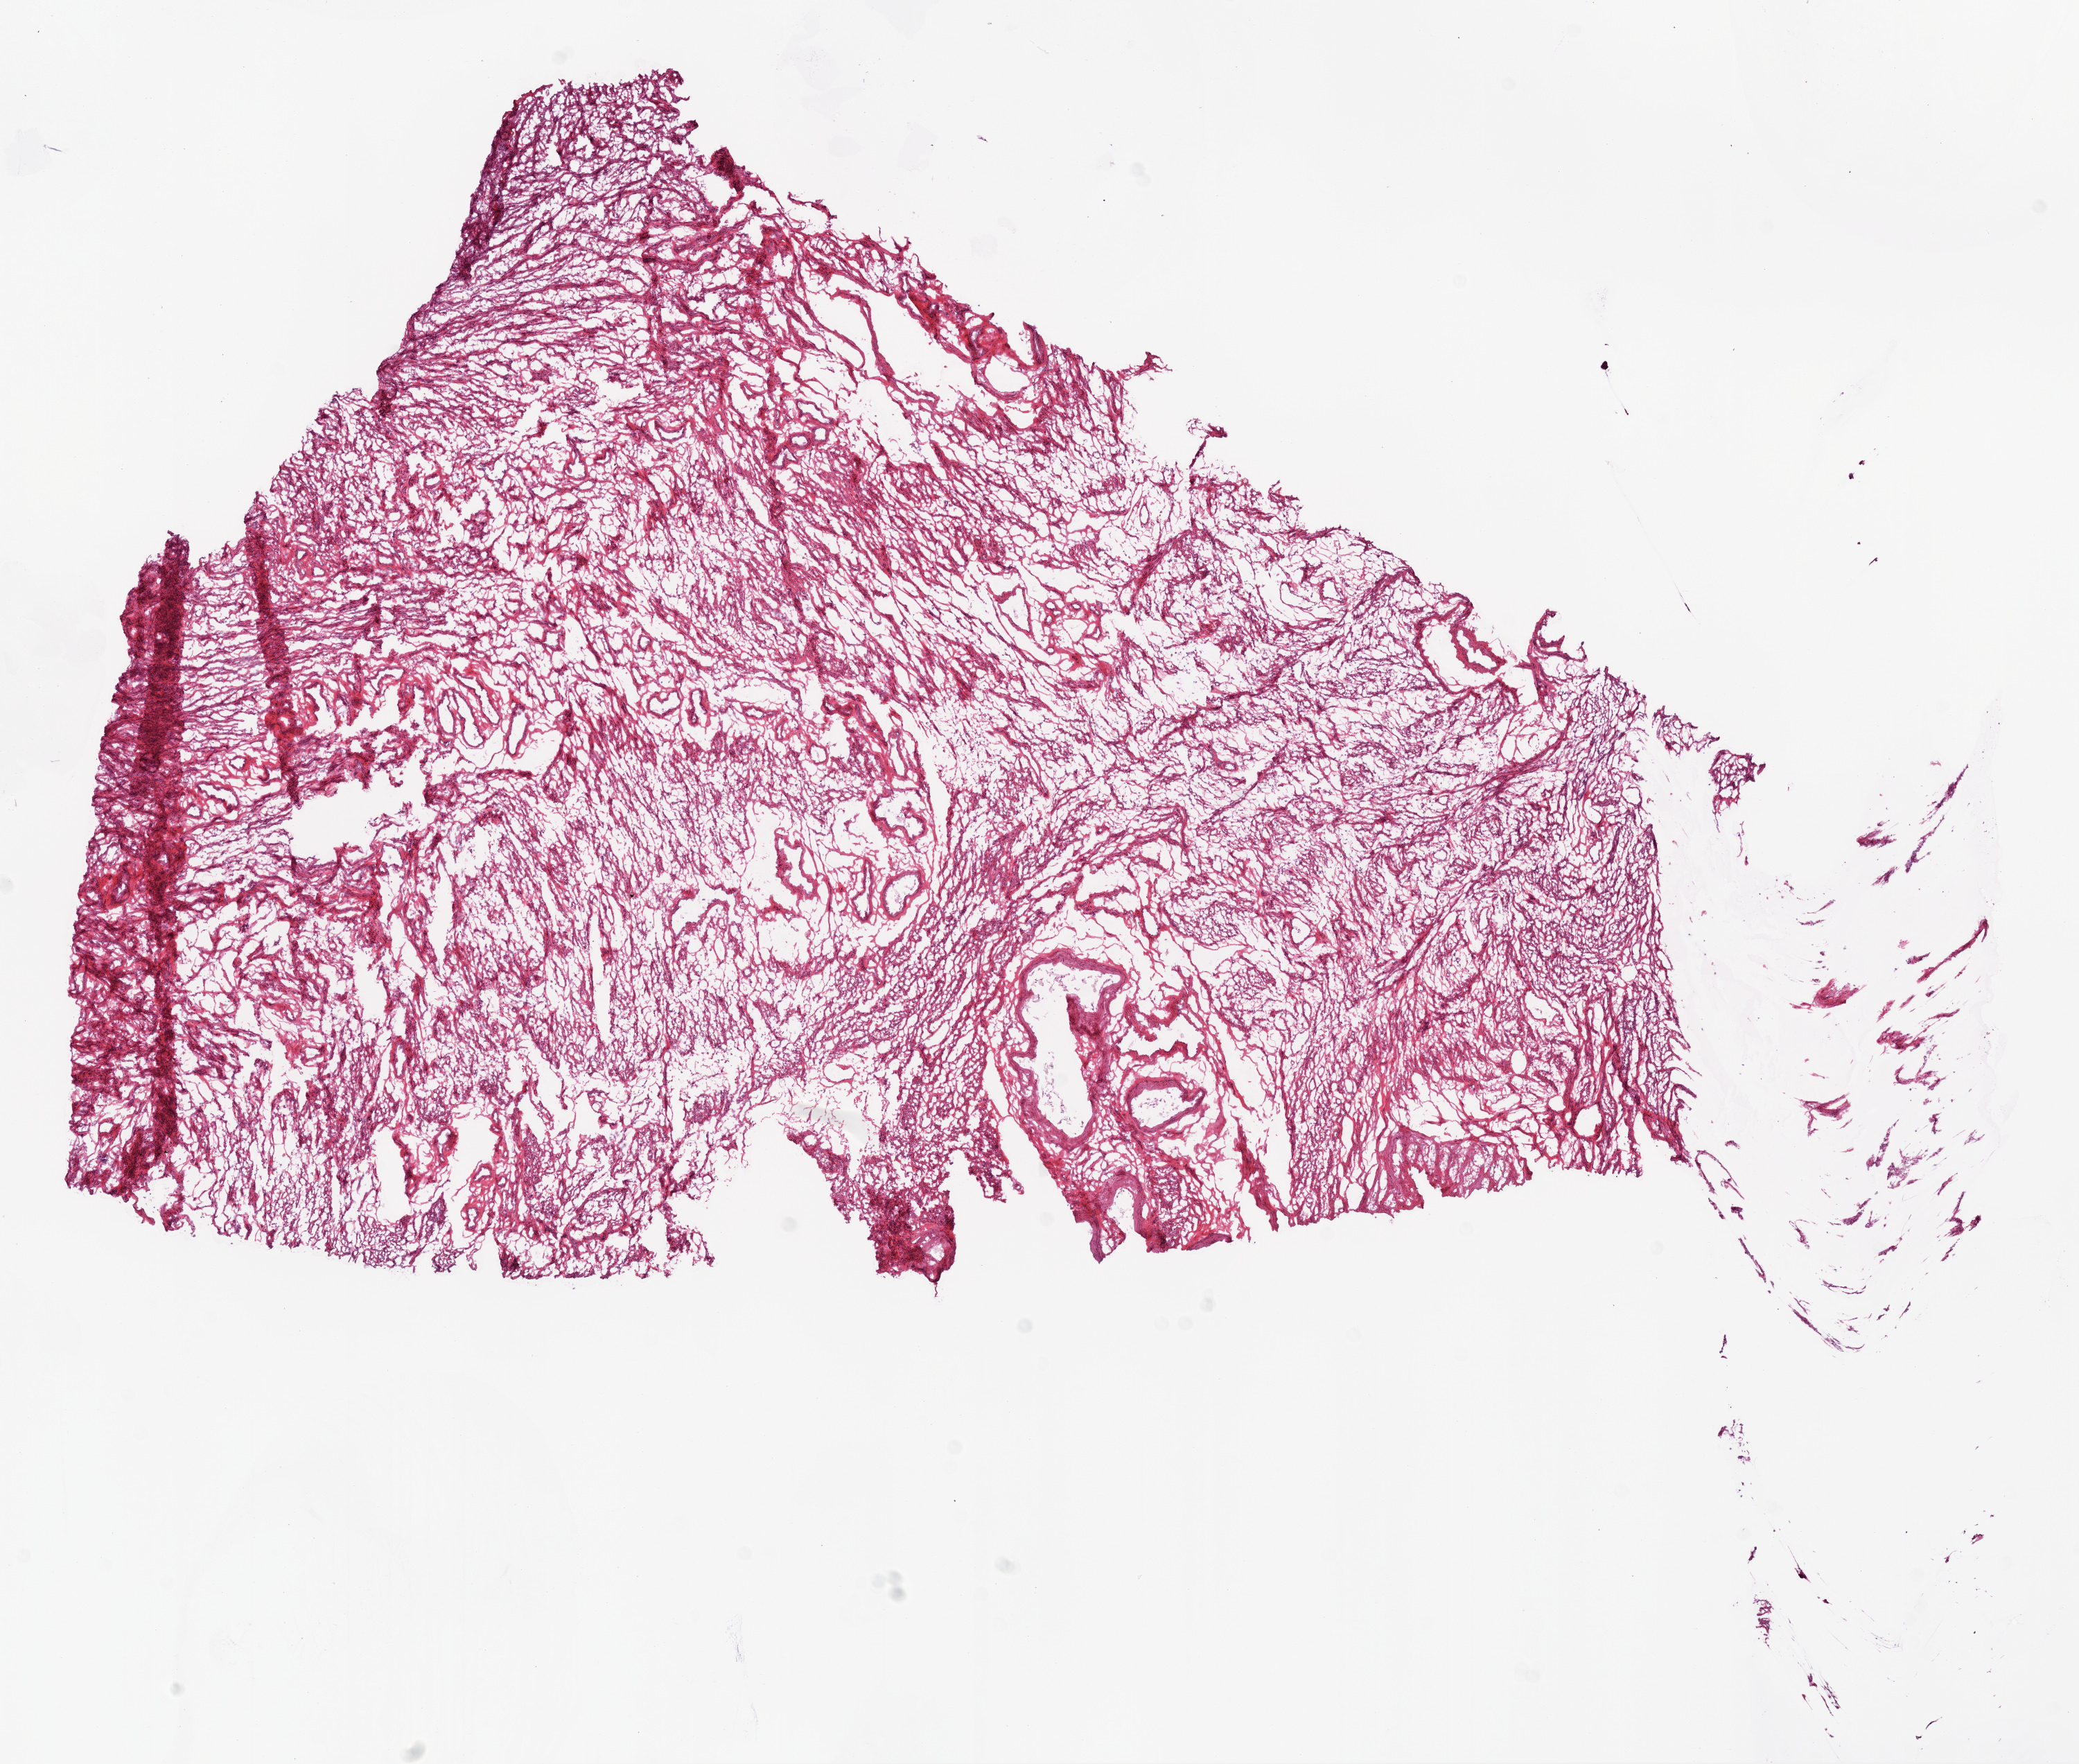
Hematoxylin and eosin (H&E) stained whole-slide image — low-resolution overview of the scanned area, about 12.0 x 10.2 mm, frozen section, solid tissue normal (non-tumour tissue) sample from the ovary. Female, age 53 years at initial diagnosis.
This section: solid tissue normal sample (biorepository sample class). Patient diagnosis: Serous cystadenocarcinoma, NOS.